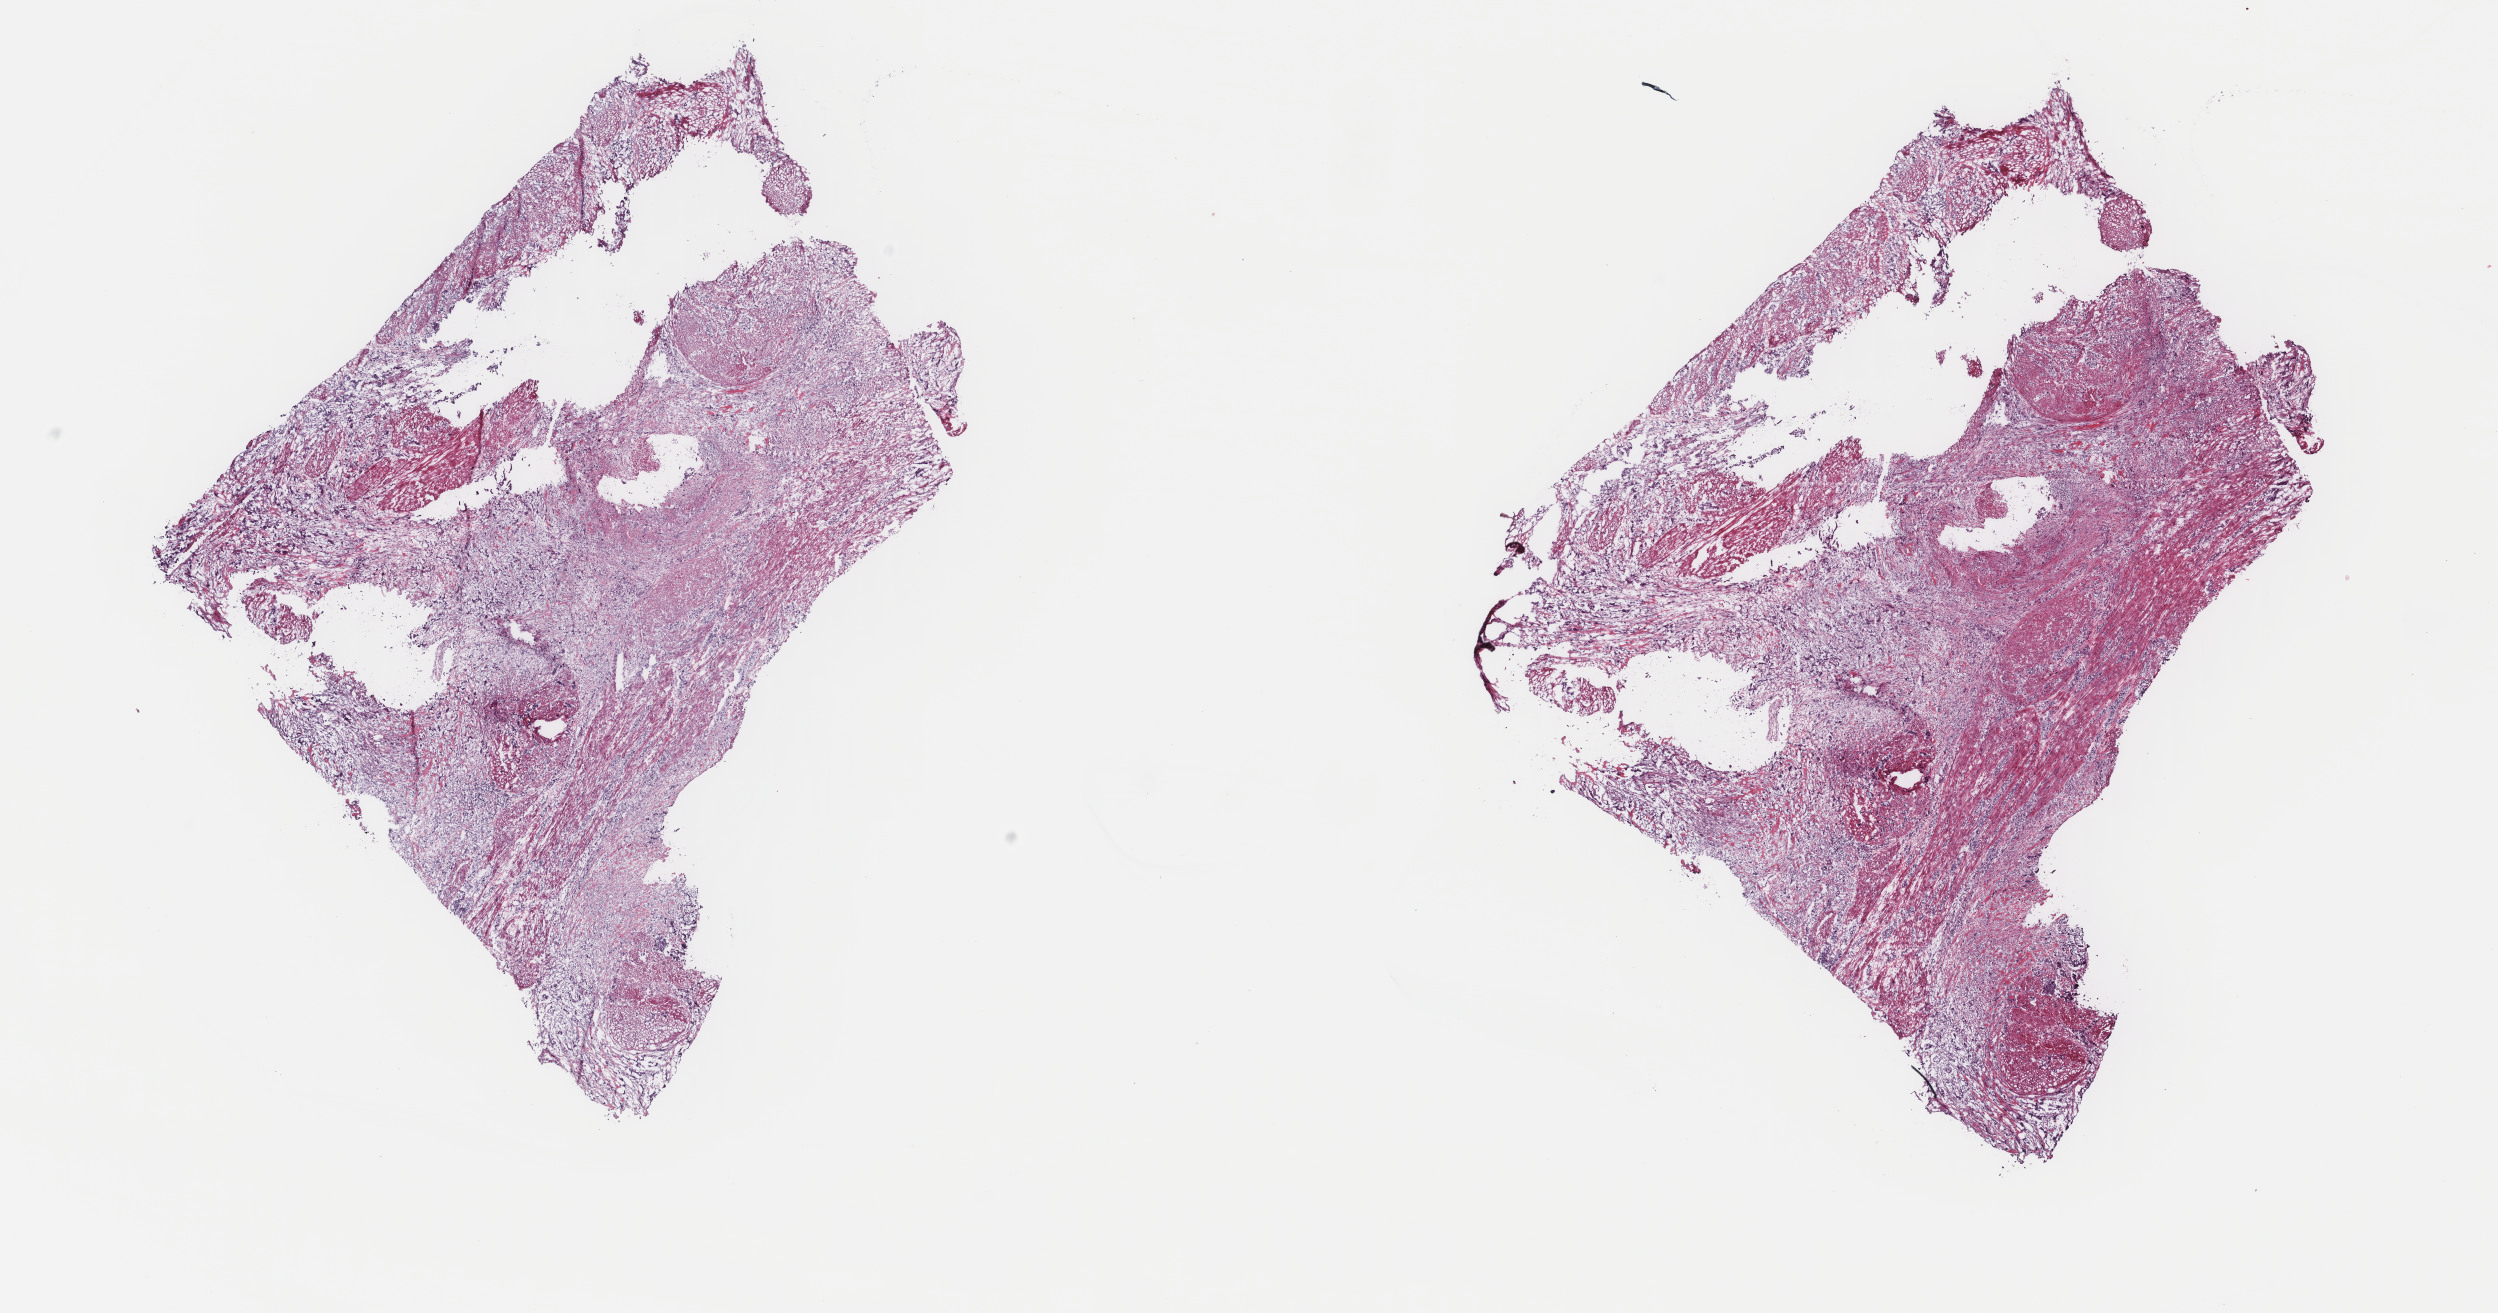
Whole-slide histology image, H&E-stained — a low-resolution overview of the entire scanned area, about 19.8 x 10.4 mm, frozen section from the top of the tissue portion, sample: primary tumour, bladder. Patient: male, age at initial diagnosis 74 years. Histologic grade: high grade. Slide review estimates, as recorded: tumour cells 75%, tumour nuclei 75%, normal cells 20%, stromal cells 5%, necrosis 0%. Infiltration values recorded for this section: lymphocyte infiltration 2%, monocyte infiltration 0%, neutrophil infiltration 0%.
Lymph nodes positive (case pathology): 0 of 14 examined. AJCC pathologic stage: III (6th edition). Histologic diagnosis: Transitional cell carcinoma (posterior wall of bladder).